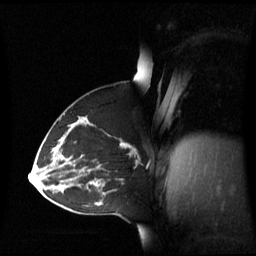
Breast MRI (dynamic contrast-enhanced), one sagittal slice; position 35 of 60 along the scan axis; dynamic contrast-enhanced series, image 2 of 3 at this slice position (ordered by acquisition); 1.5 T; TE 4.2 ms, TR 8.4 ms; 2.8 mm slice thickness; 256 × 256 image matrix, field of view 270 × 270 mm. Female patient, age 43 years. Case-level facts recorded for this patient, not image findings: setting: breast cancer imaged before/during neoadjuvant chemotherapy; receptor status: triple-negative.
Annotated regions visible in this slice (semi-automatically segmented with operator editing):
- analysis volume of interest (the breast-tissue region the enhancement analysis was run in; not a lesion): box from (x=55, y=124) to (x=139, y=173) px
- tumour enhancement mask (voxels above the 70 % enhancement threshold inside the analysis volume of interest): (x=120, y=142)–(x=137, y=153)